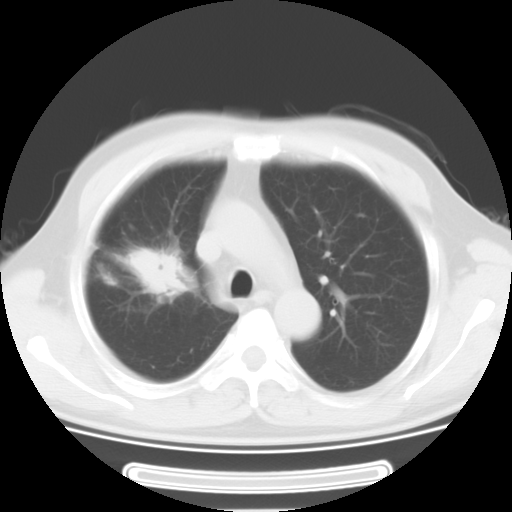
Chest CT, one axial slice; slice 21 of 29 in the series (ordered by position); reconstruction kernel STANDARD; lung window (W 1500 / L -600 HU); 10 mm slice thickness; 512 × 512 image matrix, field of view 350 × 350 mm. Male patient, age 46 years. Case-level facts recorded for this patient, not image findings: clinical TNM (as recorded): T3 N0 M1b.
Annotated regions visible in this slice (bounding box drawn by a radiologist):
- lung tumour (recorded histology: adenocarcinoma): bounding box <112,230,185,305> (left, top, right, bottom; pixels)